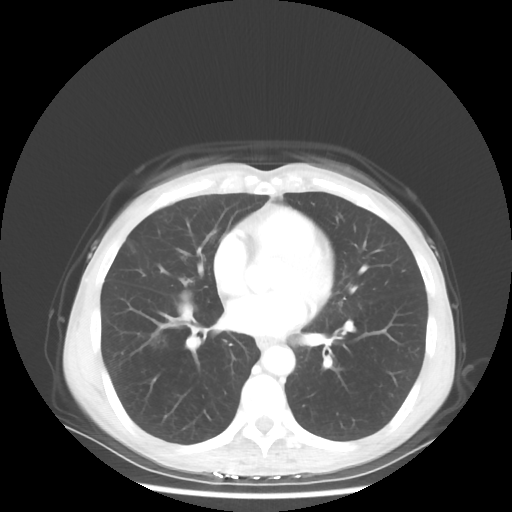
Chest CT, one axial slice; position 24 of 56 along the scan axis; reconstruction kernel STANDARD; lung window (W 1500 / L -600 HU); 5 mm slice thickness; 512 × 512 image matrix, field of view 360 × 360 mm. Patient: female, 57 years. From the clinical record (not read from this slice): clinical TNM (as recorded): T1c N3 M1a; histopathological grade: G3.
Structures marked on this image (rectangle marked by the reading radiologist):
- lung tumour (recorded histology: adenocarcinoma): bounding box (x1, y1, x2, y2) in pixels: (175, 302, 198, 329)